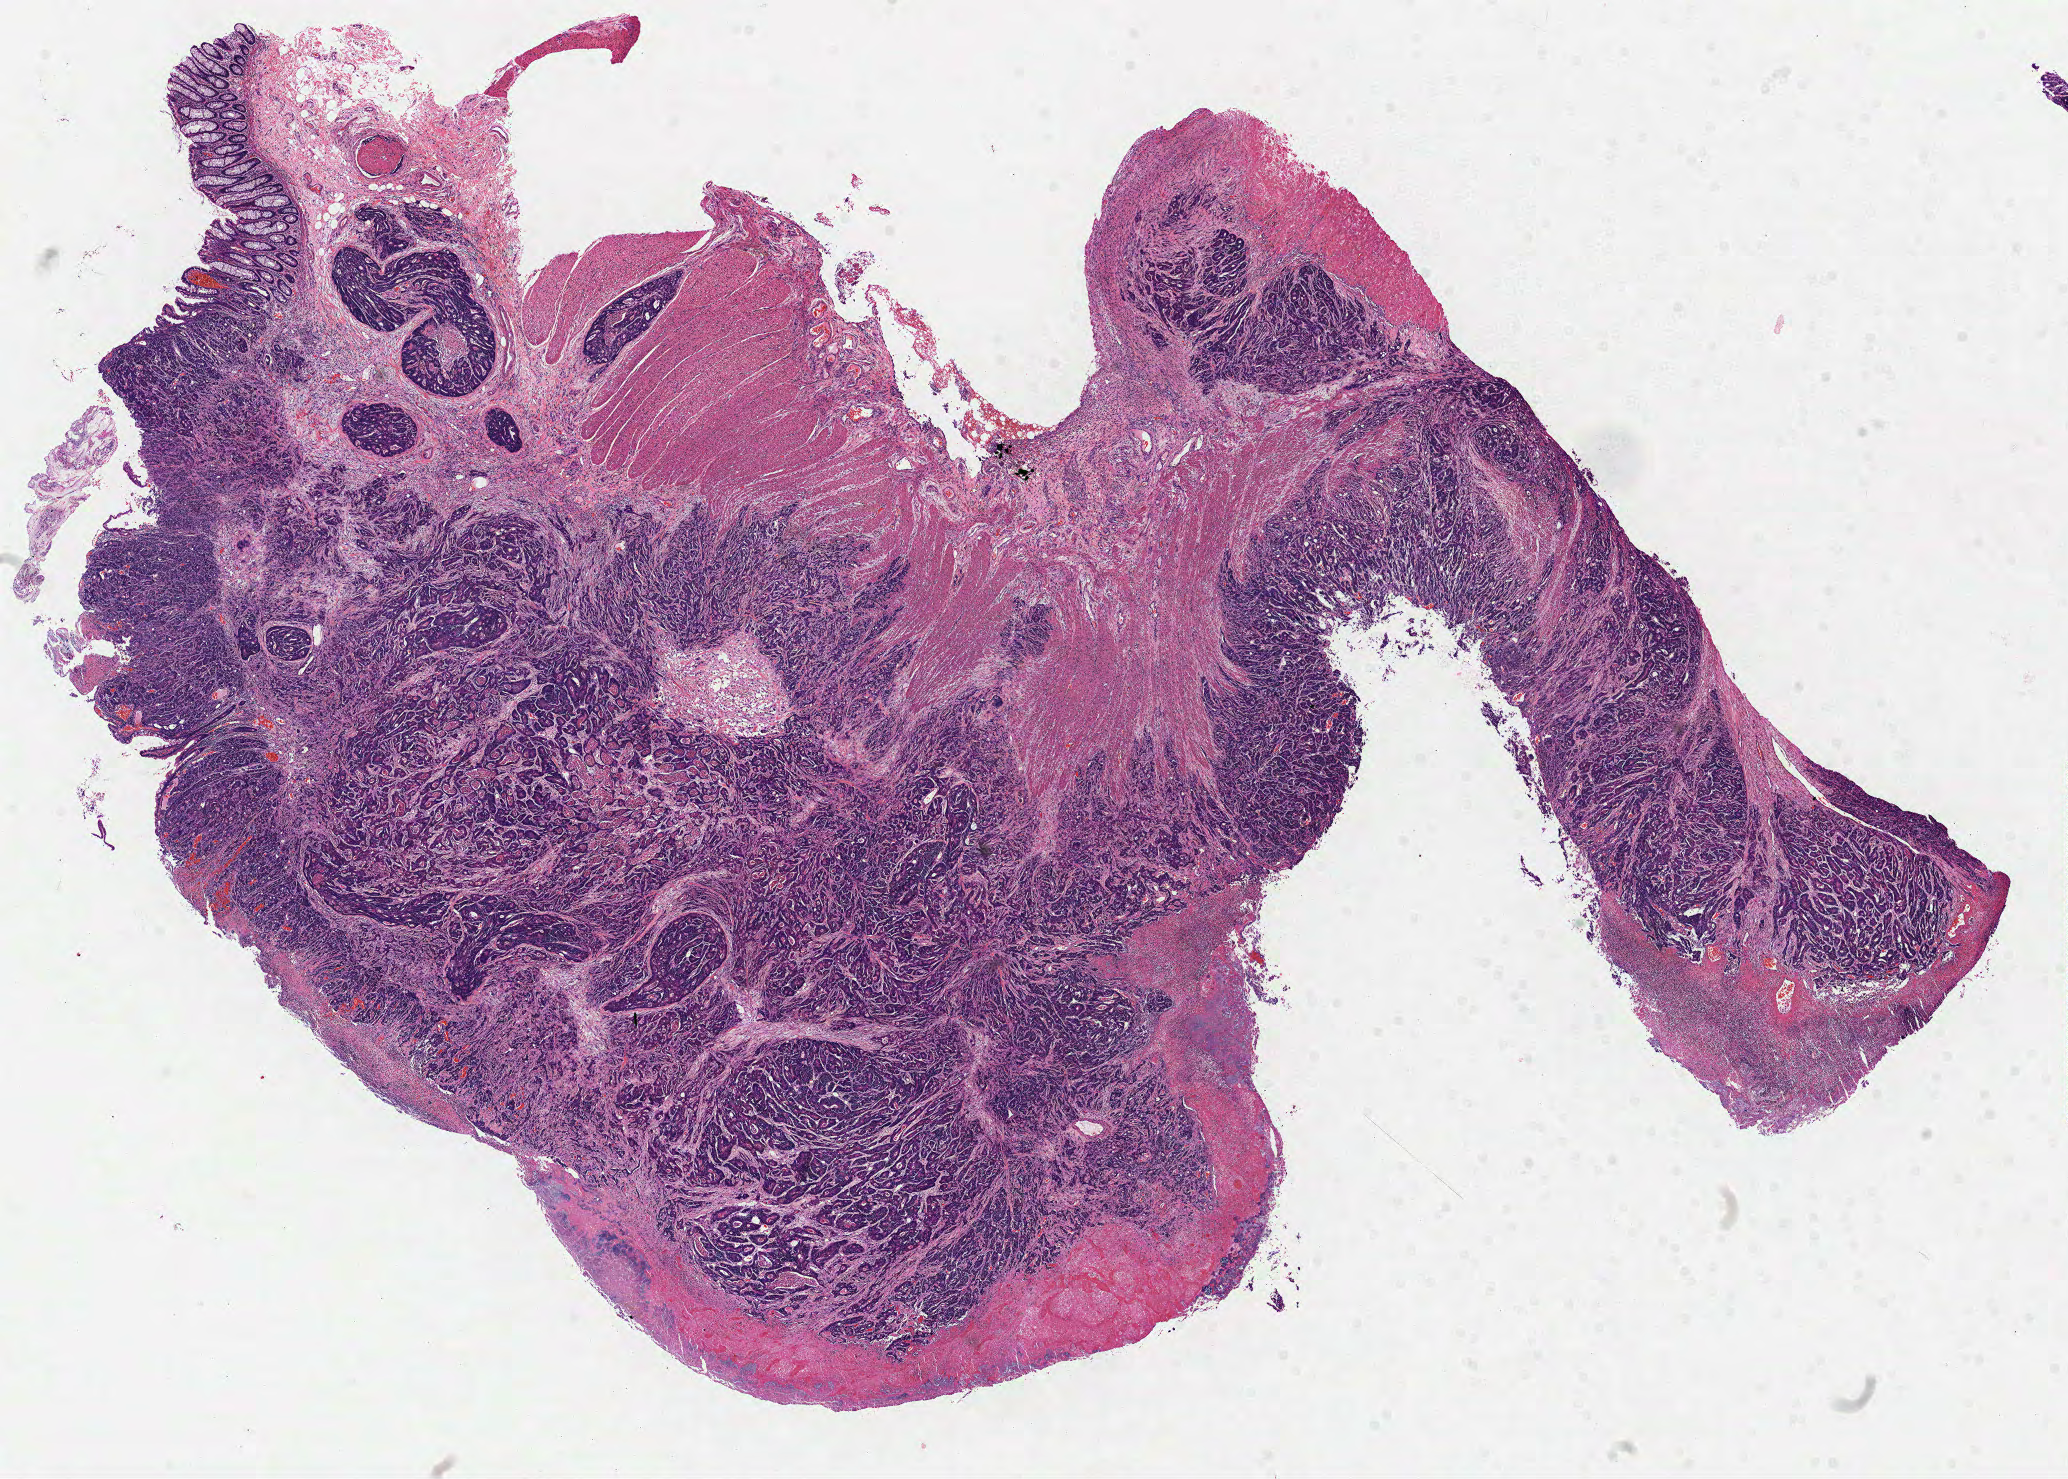
Digitized H&E-stained tissue section (whole slide) — whole scanned area (about 16.7 x 11.9 mm, from a 40x scan) shown as a low-resolution overview; formalin-fixed paraffin-embedded (FFPE) diagnostic section; sample: primary tumour, colon. Female, age 59 years at initial diagnosis.
Diagnosis: Adenocarcinoma, NOS.